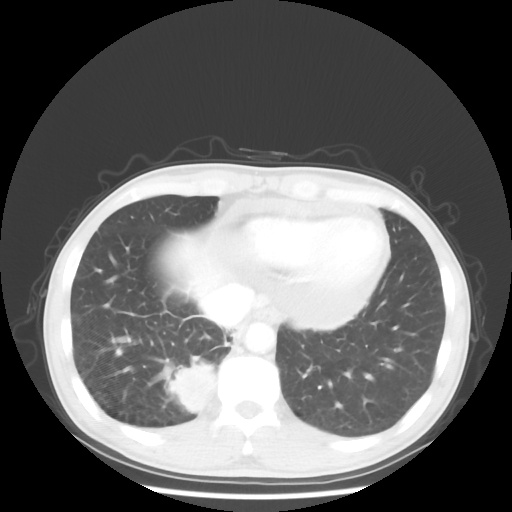
Chest CT, one axial slice. Position 12 of 58 along the scan axis. Reconstruction kernel STANDARD. Lung window (W 1500 / L -600 HU). 5 mm slice thickness. 512 × 512 image matrix, field of view 360 × 360 mm. Patient: male, 56 years. Case-level facts recorded for this patient, not image findings: clinical TNM (as recorded): T2 N1 M1; histopathological grade: G1.
Annotated regions visible in this slice (rectangle marked by the reading radiologist):
- lung tumour (recorded histology: adenocarcinoma): box from (x=168, y=356) to (x=219, y=421) px